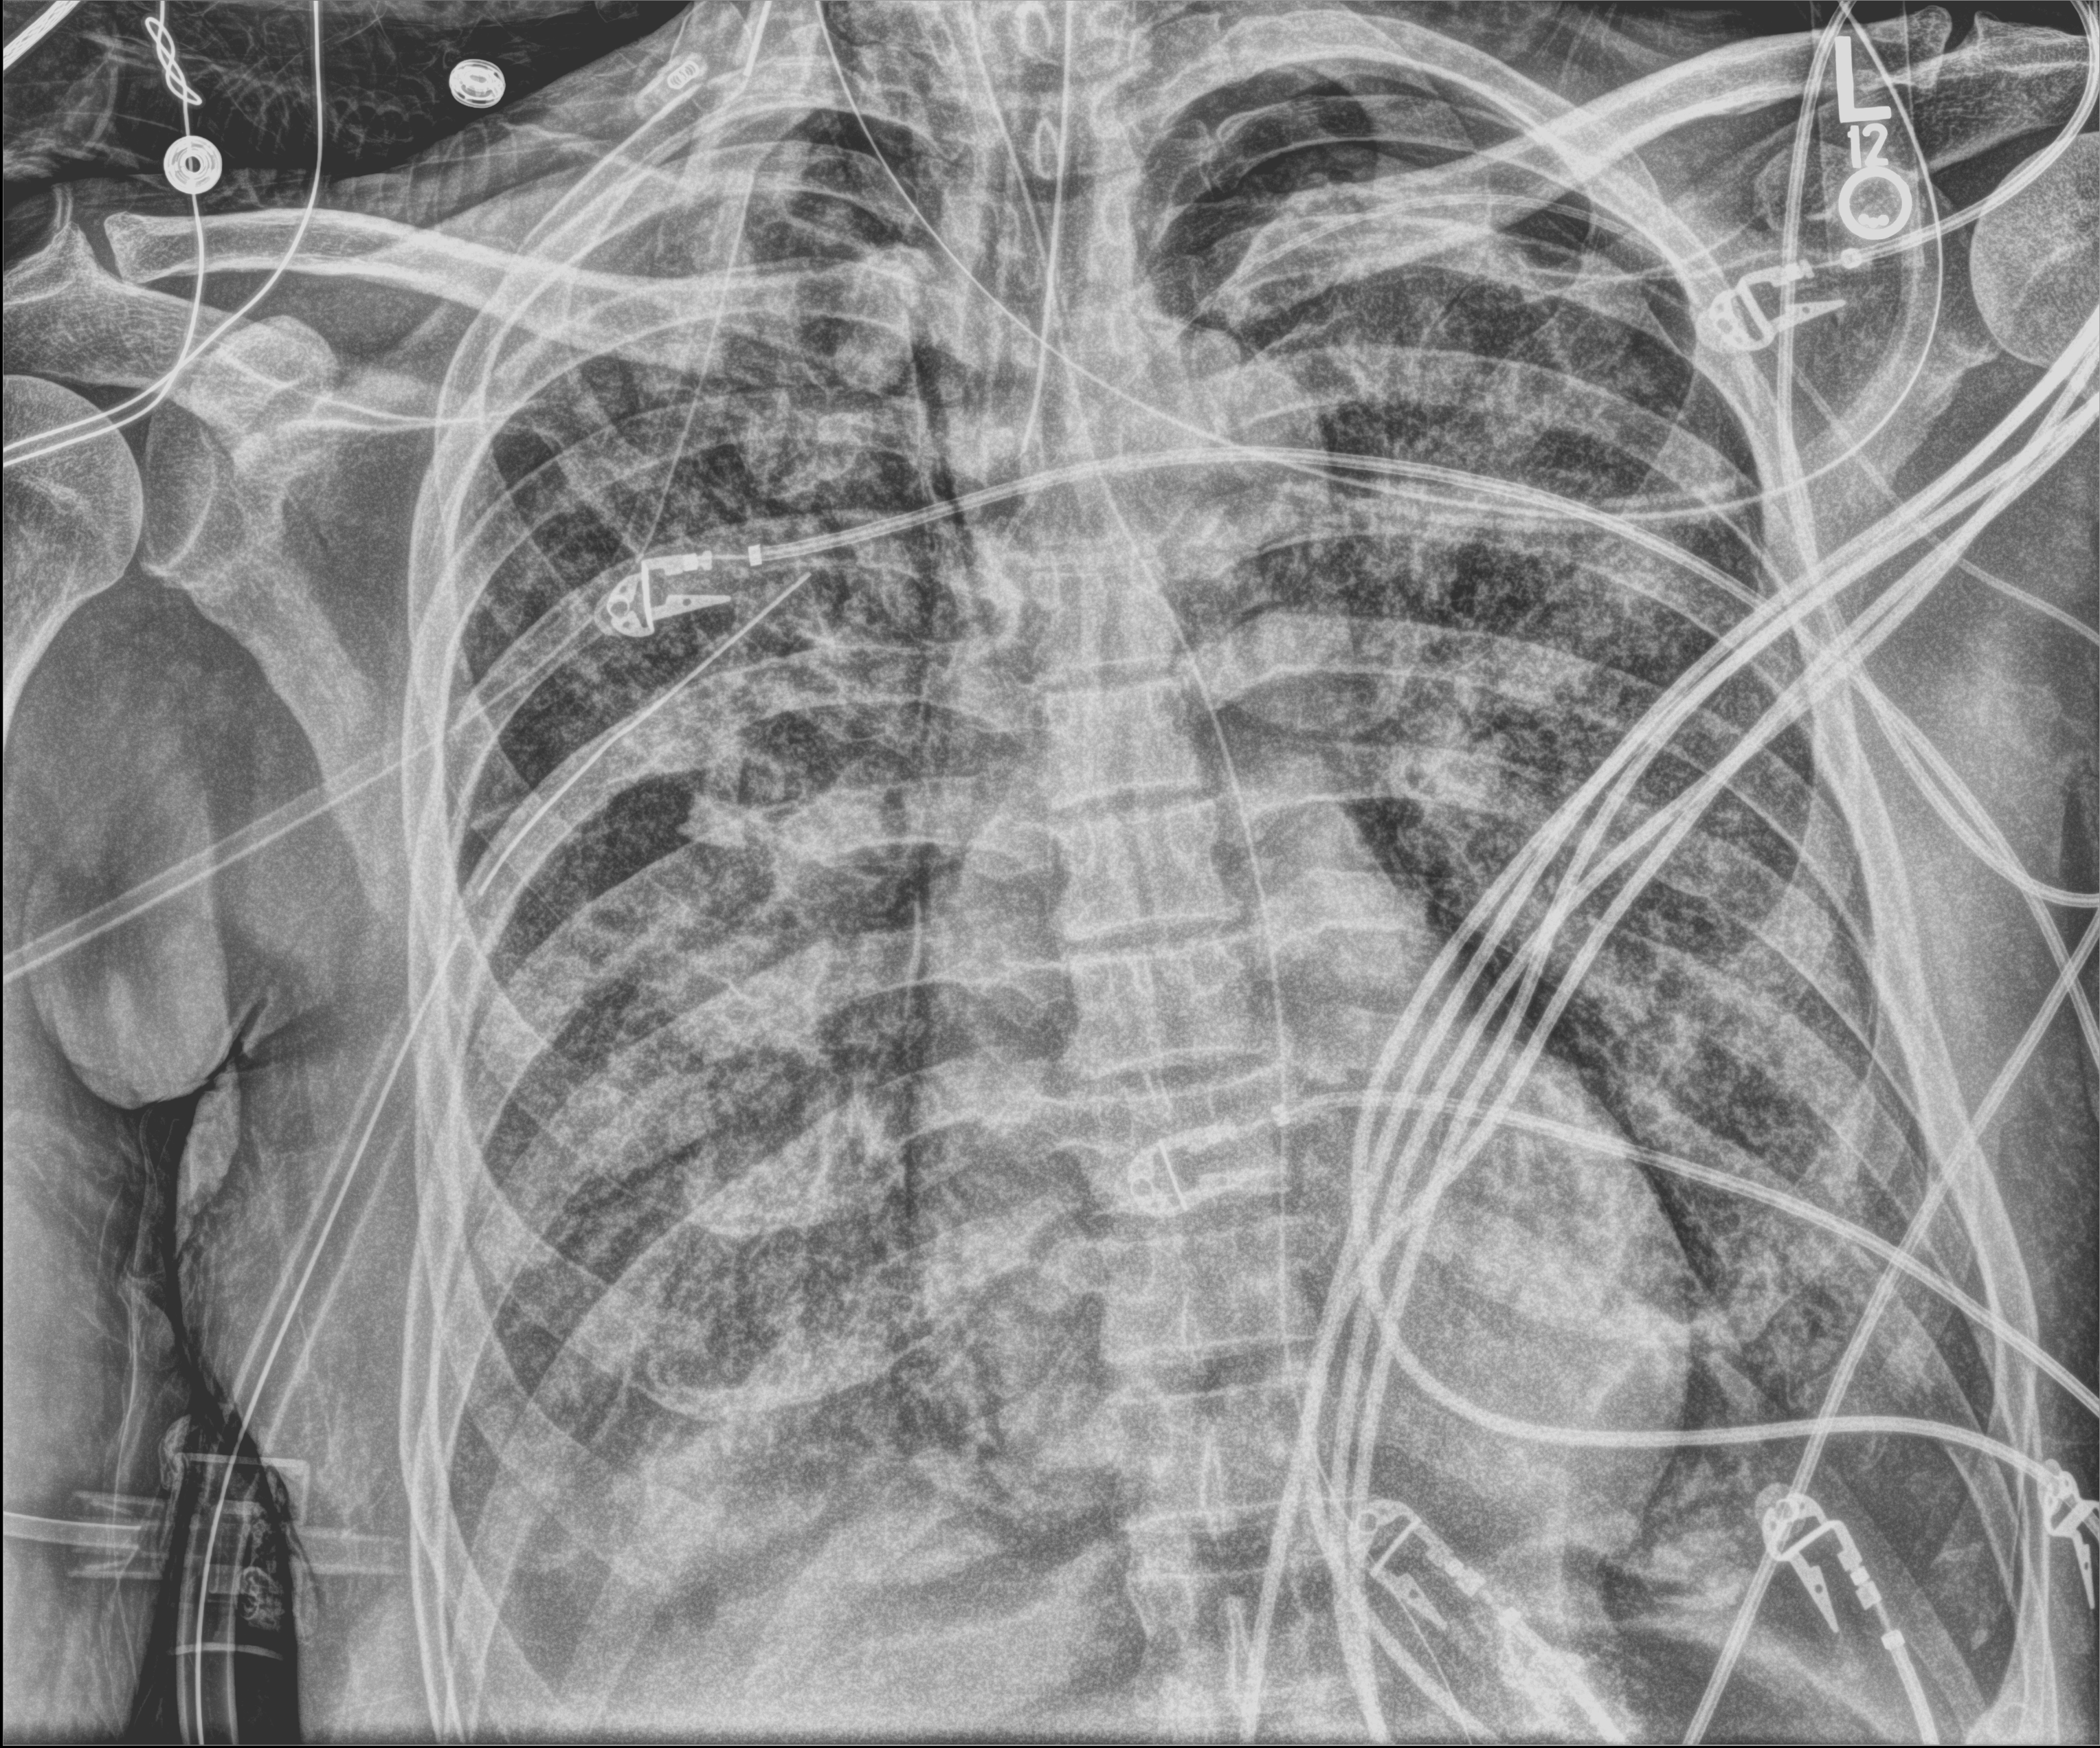
Chest X-ray (portable), anteroposterior (AP) projection. Male patient hospitalised with COVID-19, age 60–74 years.
Admission-level facts for this patient (not findings on this image; timing relative to this image not recorded): smoking status (admission record): former; COPD (admission record): no; mechanically ventilated during this hospital stay: yes.